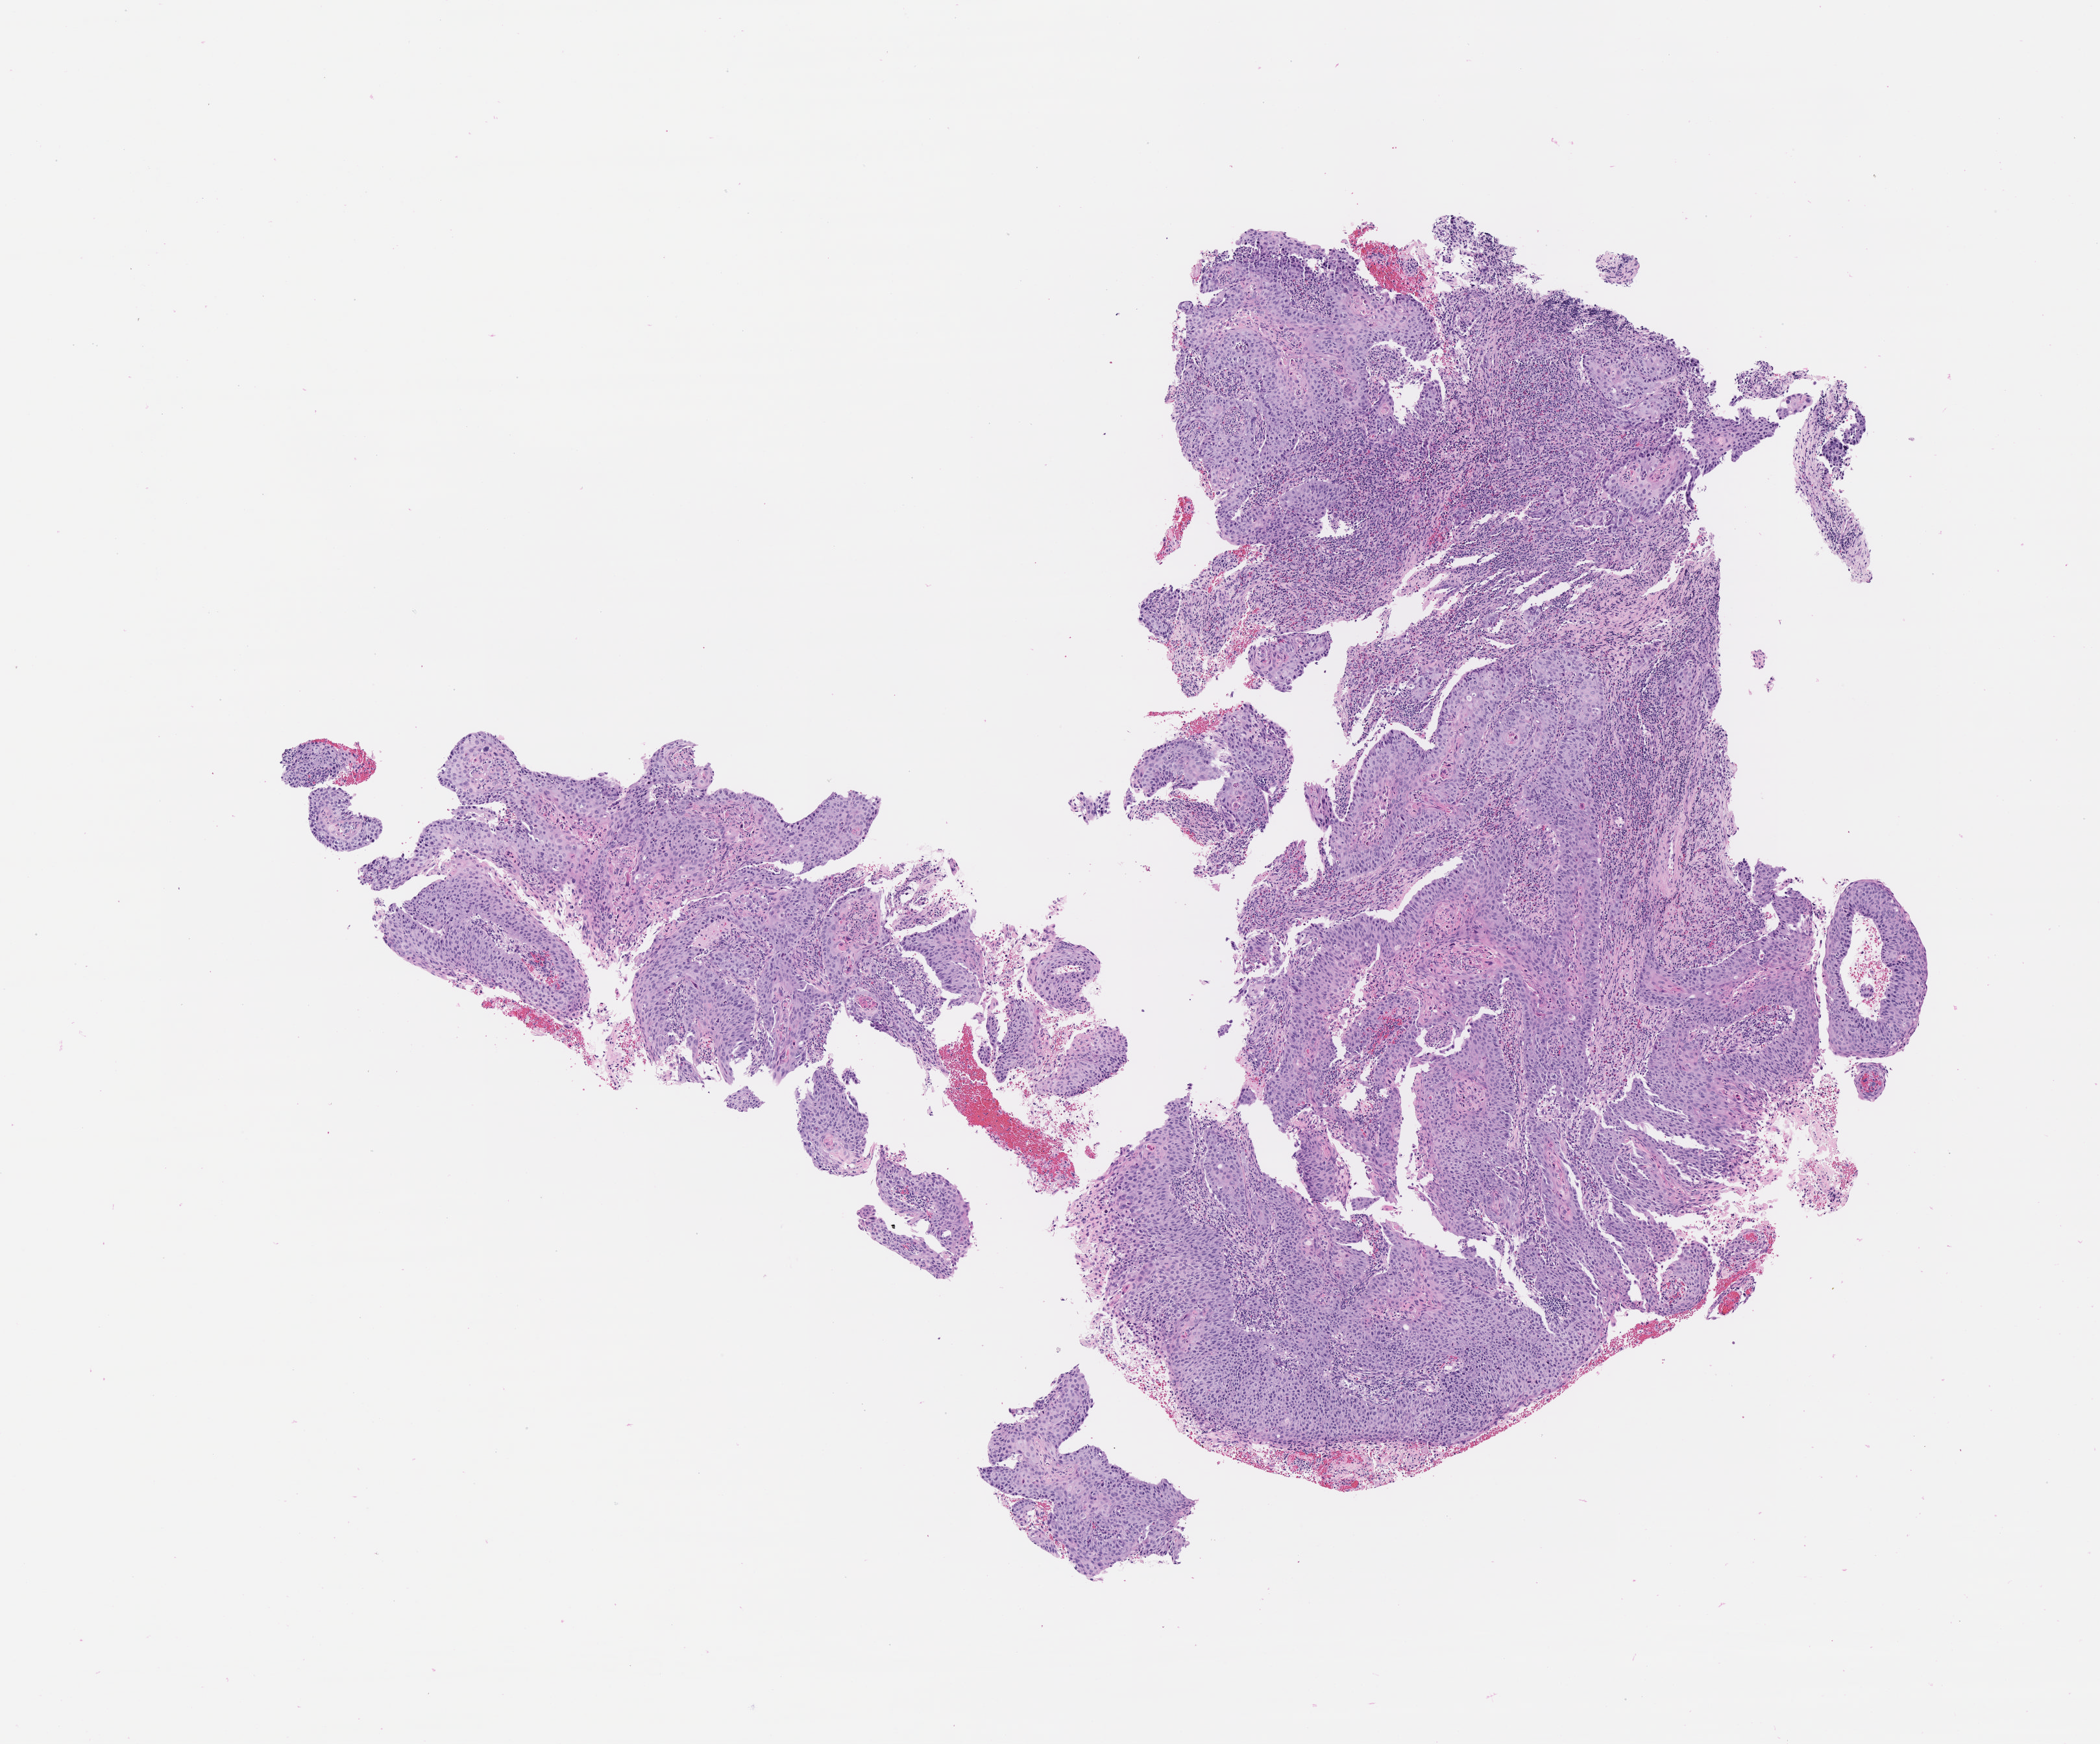
Whole-slide image, hematoxylin and eosin (H&E) stain, a low-resolution overview of the entire scanned area, about 6.5 x 5.4 mm; specimen: tumor tissue; site: cervix. Patient: female, aged 60.
- diagnosis: Squamous cell carcinoma, keratinizing, NOS